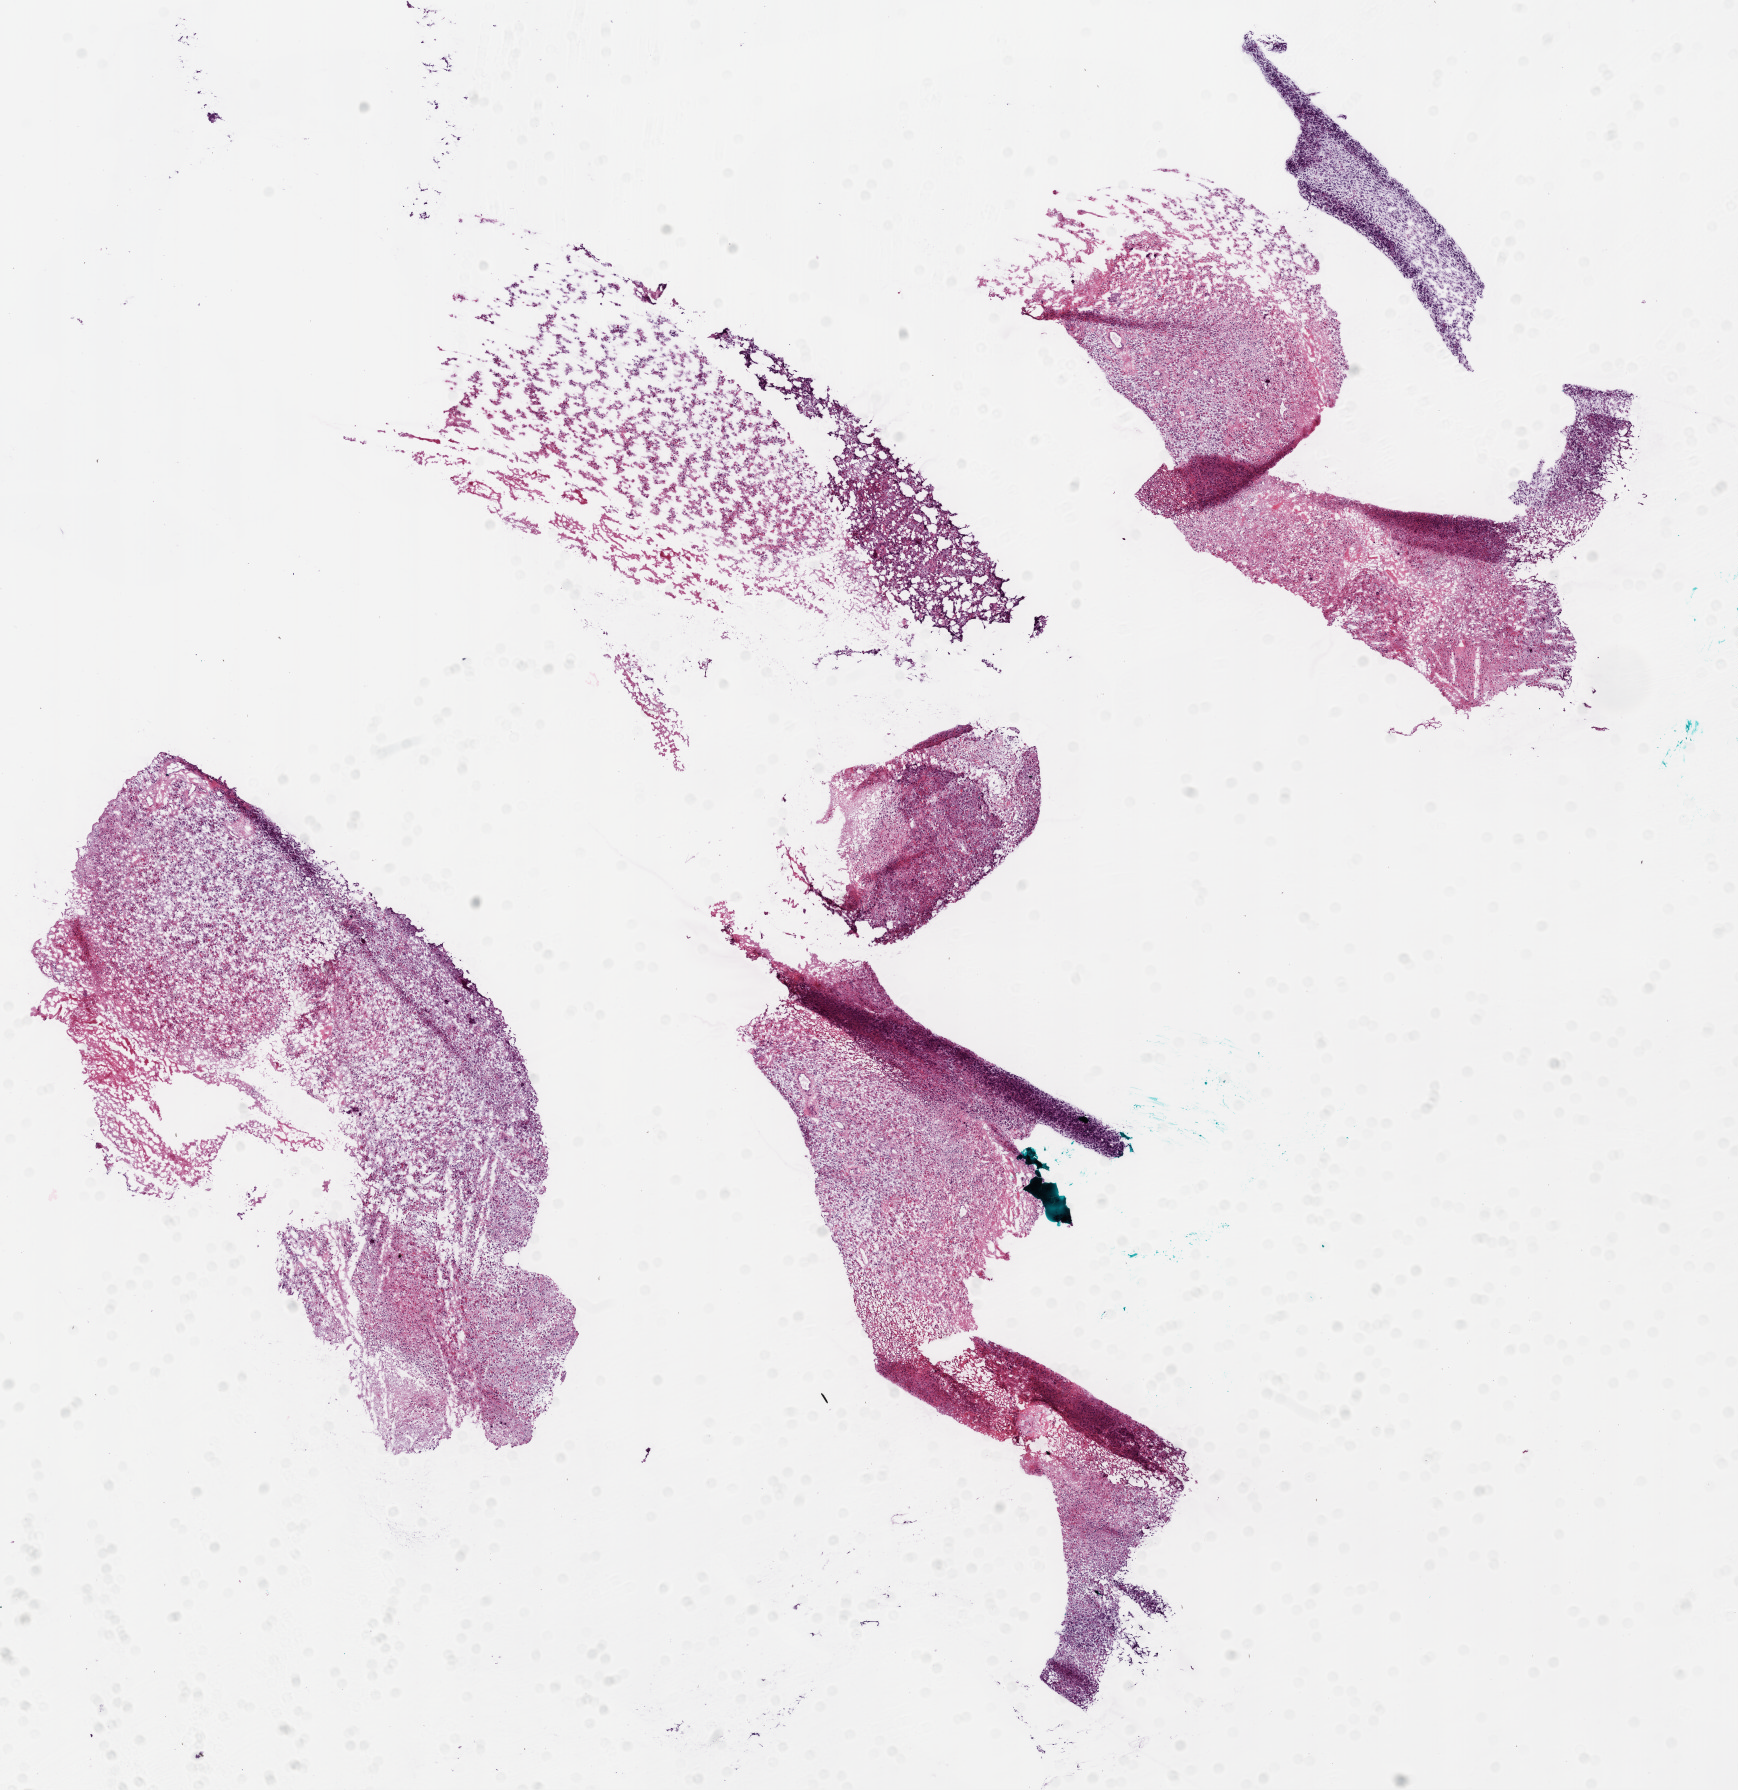
Hematoxylin and eosin (H&E) stained whole-slide image, shown as a low-resolution overview of the whole scanned area (about 14.0 x 14.4 mm, acquisition: 20x scan), frozen section from the bottom of the tissue portion, sample: primary tumour, brain. Male, age 54 years at initial diagnosis. Pathologist review of this section (percent, as recorded): tumour cells 90%, tumour nuclei 95%, stromal cells 5%, necrosis 5%.
Diagnosis: Glioblastoma.